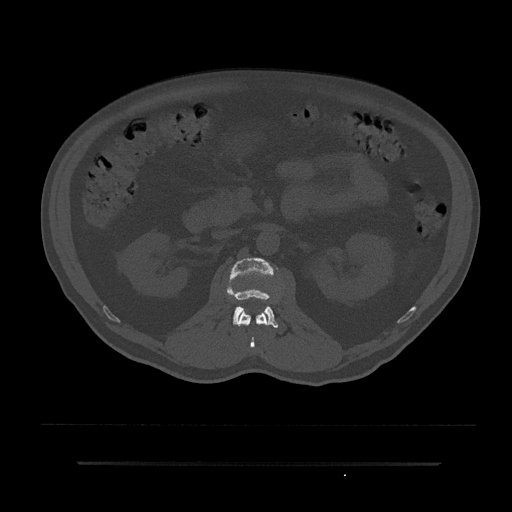
CT including the spine, one axial slice; position 107 of 797 along the scan axis; 120 kVp; bone window (W 1800 / L 400 HU); 512 × 512 image matrix, field of view 464 × 464 mm. Patient: male, 59 years. From the clinical record (not read from this slice): primary cancer: bile ducts; vertebrae with lytic lesions (as recorded): T10.
Annotated regions visible in this slice (semi-automatic segmentation, software-assisted and operator-edited):
- L1 vertebra: box from (x=238, y=311) to (x=268, y=348) px
- L2 vertebra: (x=227, y=258)–(x=278, y=328)